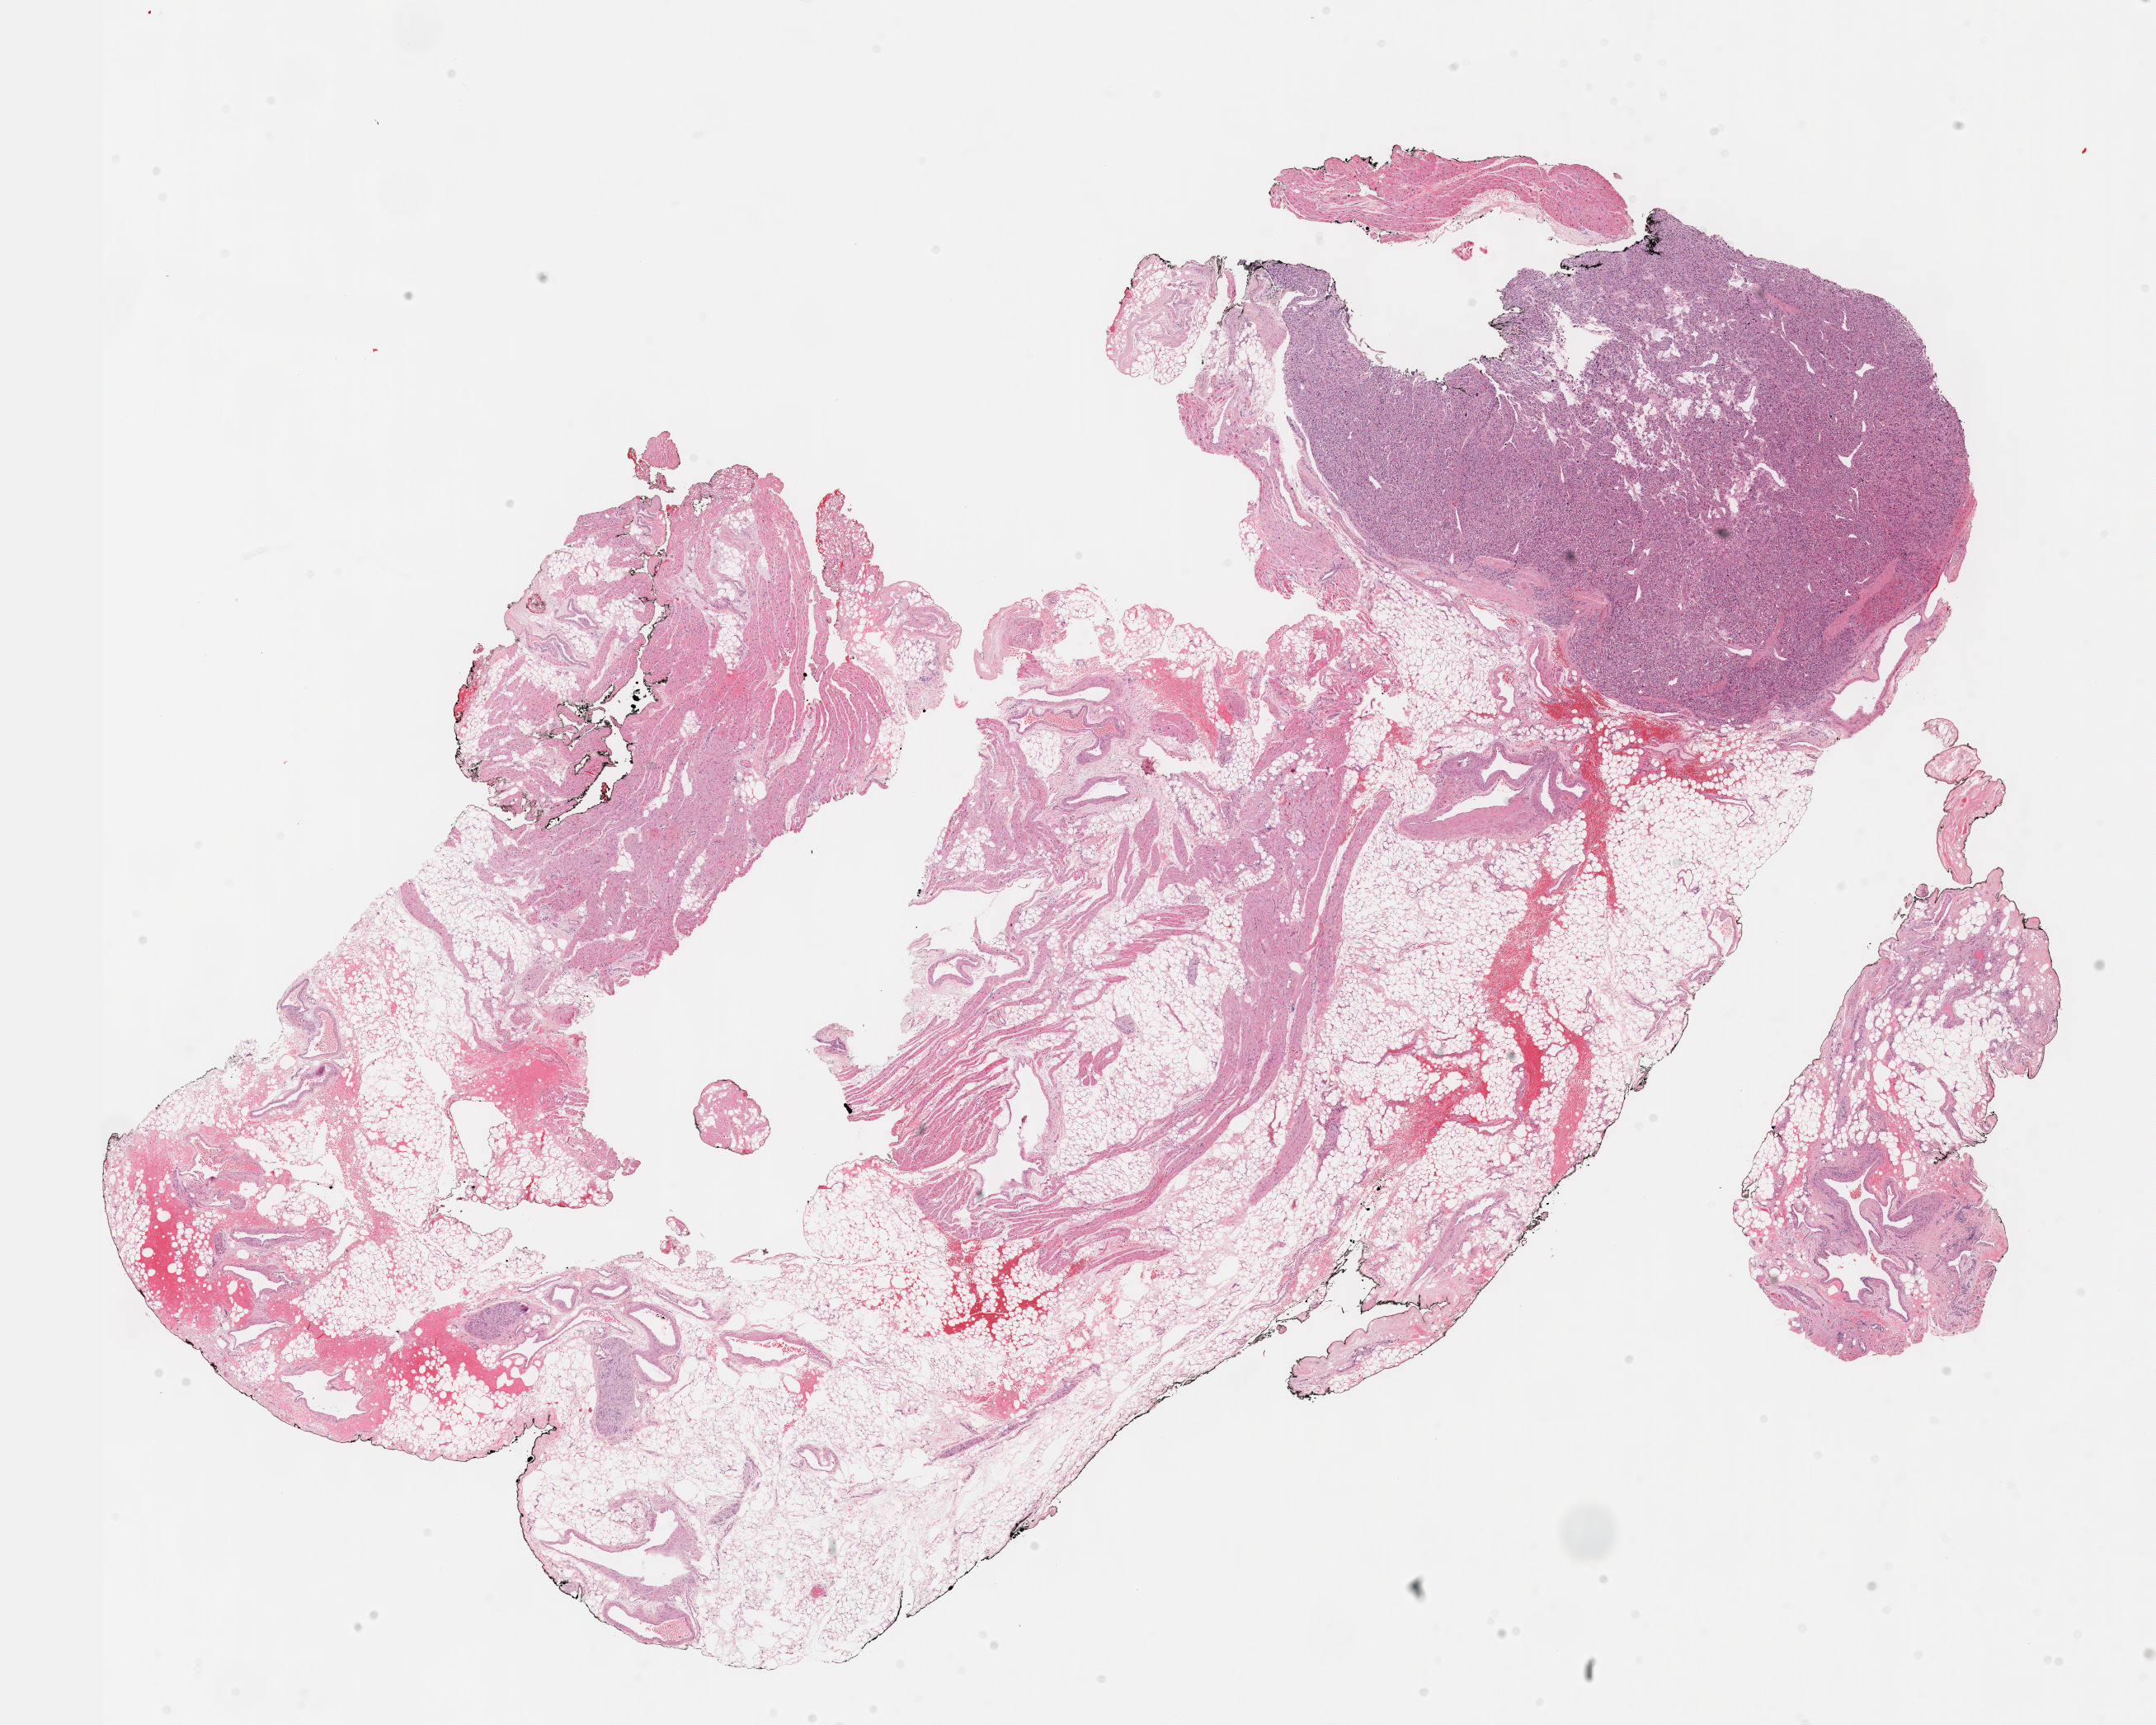
Whole-slide histology image, H&E-stained, a low-resolution overview of the entire scanned area, about 21.1 x 16.9 mm (acquisition: 40x scan), formalin-fixed paraffin-embedded (FFPE) diagnostic section, primary tumour sample. Male, age 33 years at initial diagnosis.
Diagnosis: Extra-adrenal paraganglioma, NOS (thorax, NOS).